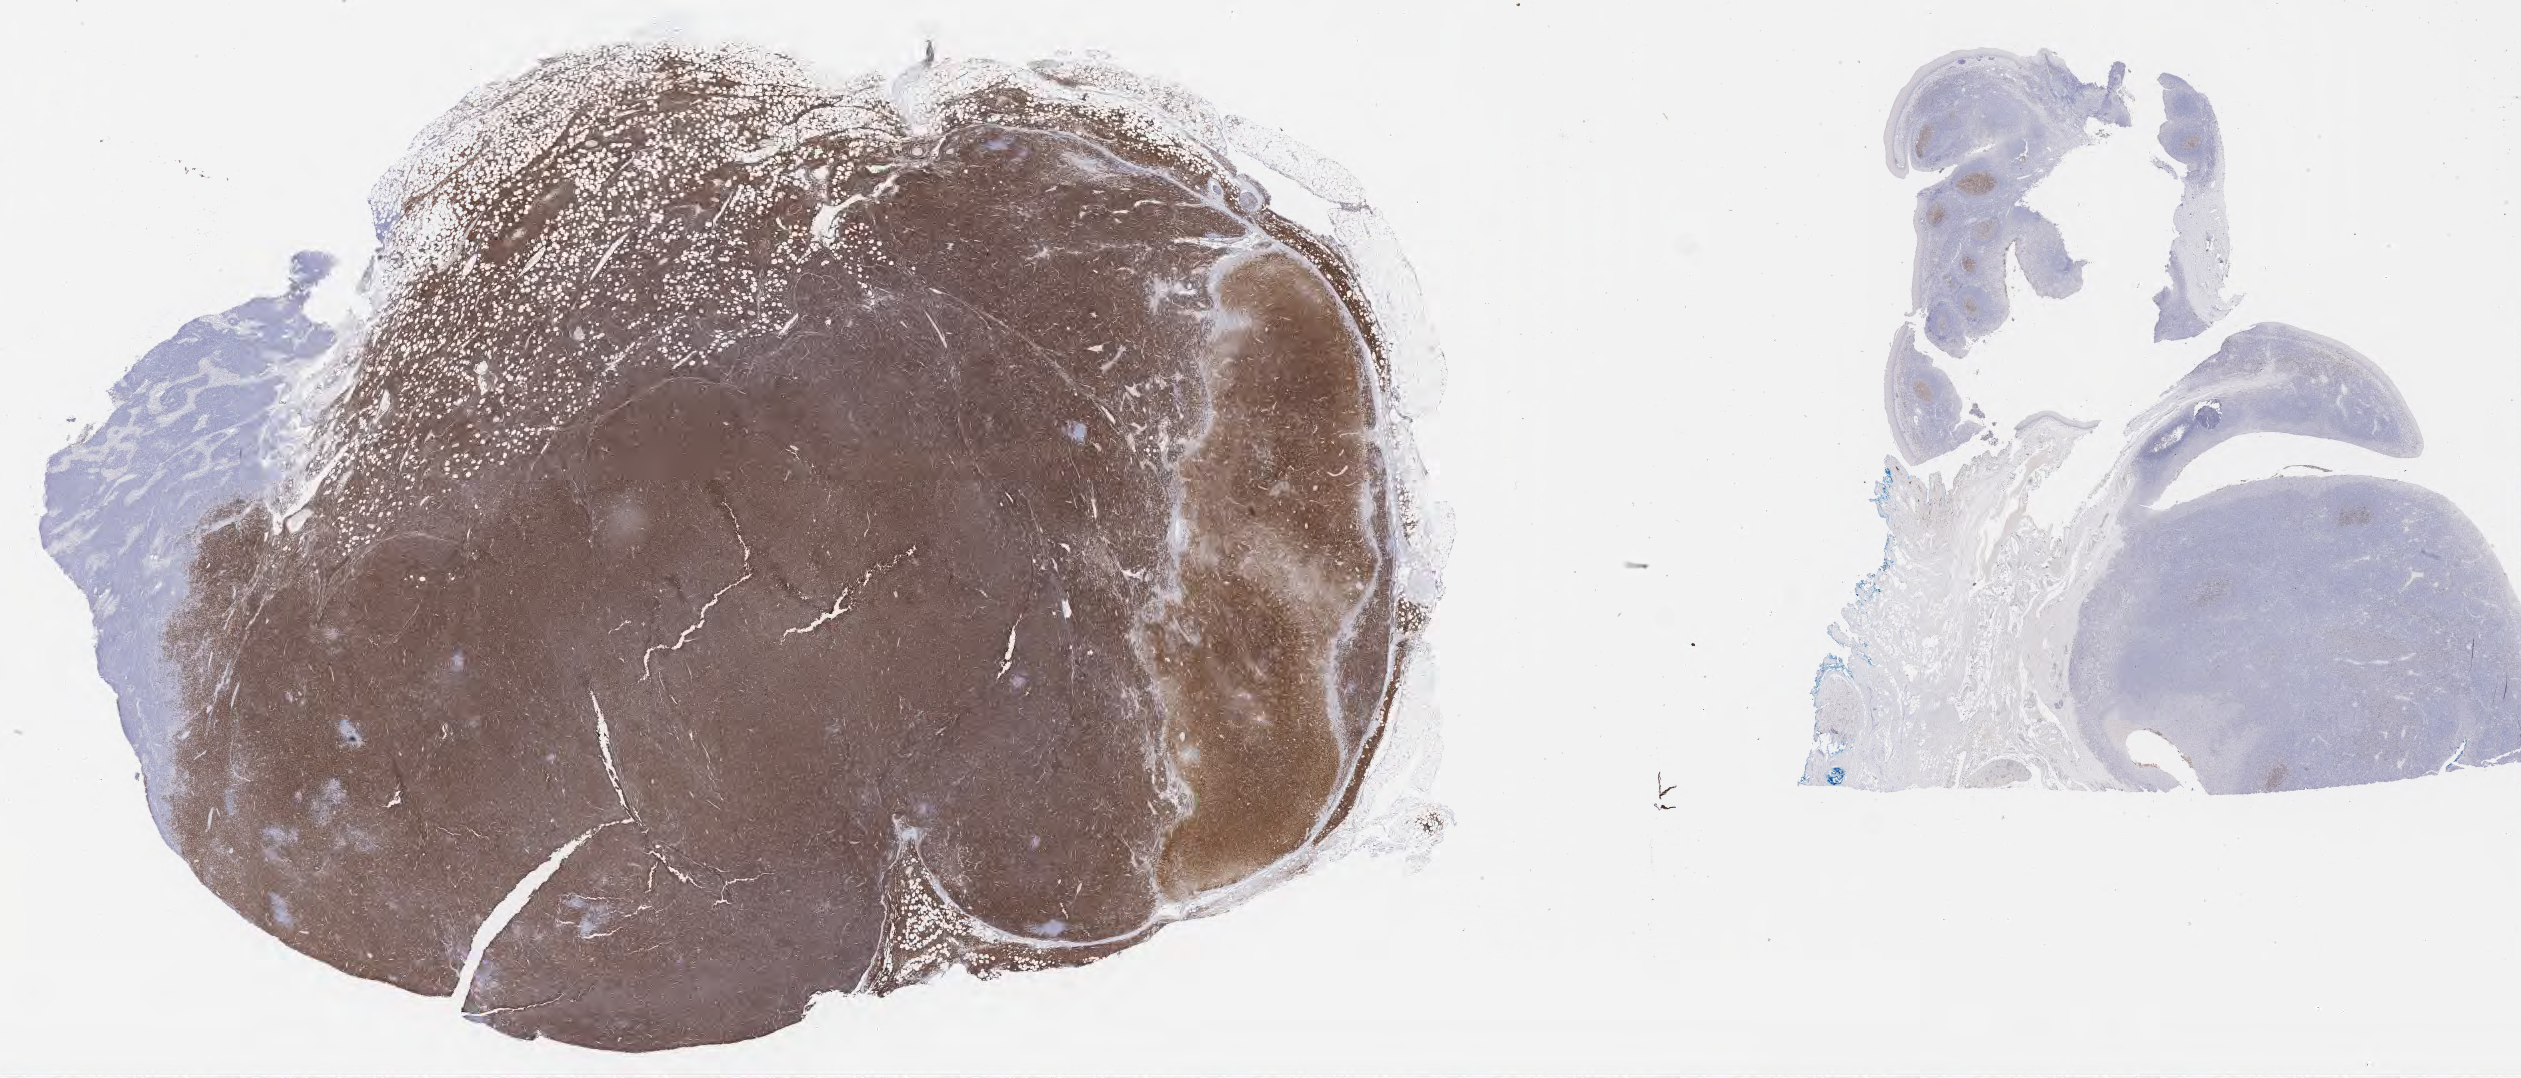
IHC for CD10, whole-slide image — shown as a low-resolution overview of the whole scanned area (about 40.8 x 17.4 mm), tumor tissue. Patient: male, age 57 years.
Histologic diagnosis: Burkitt lymphoma, NOS.